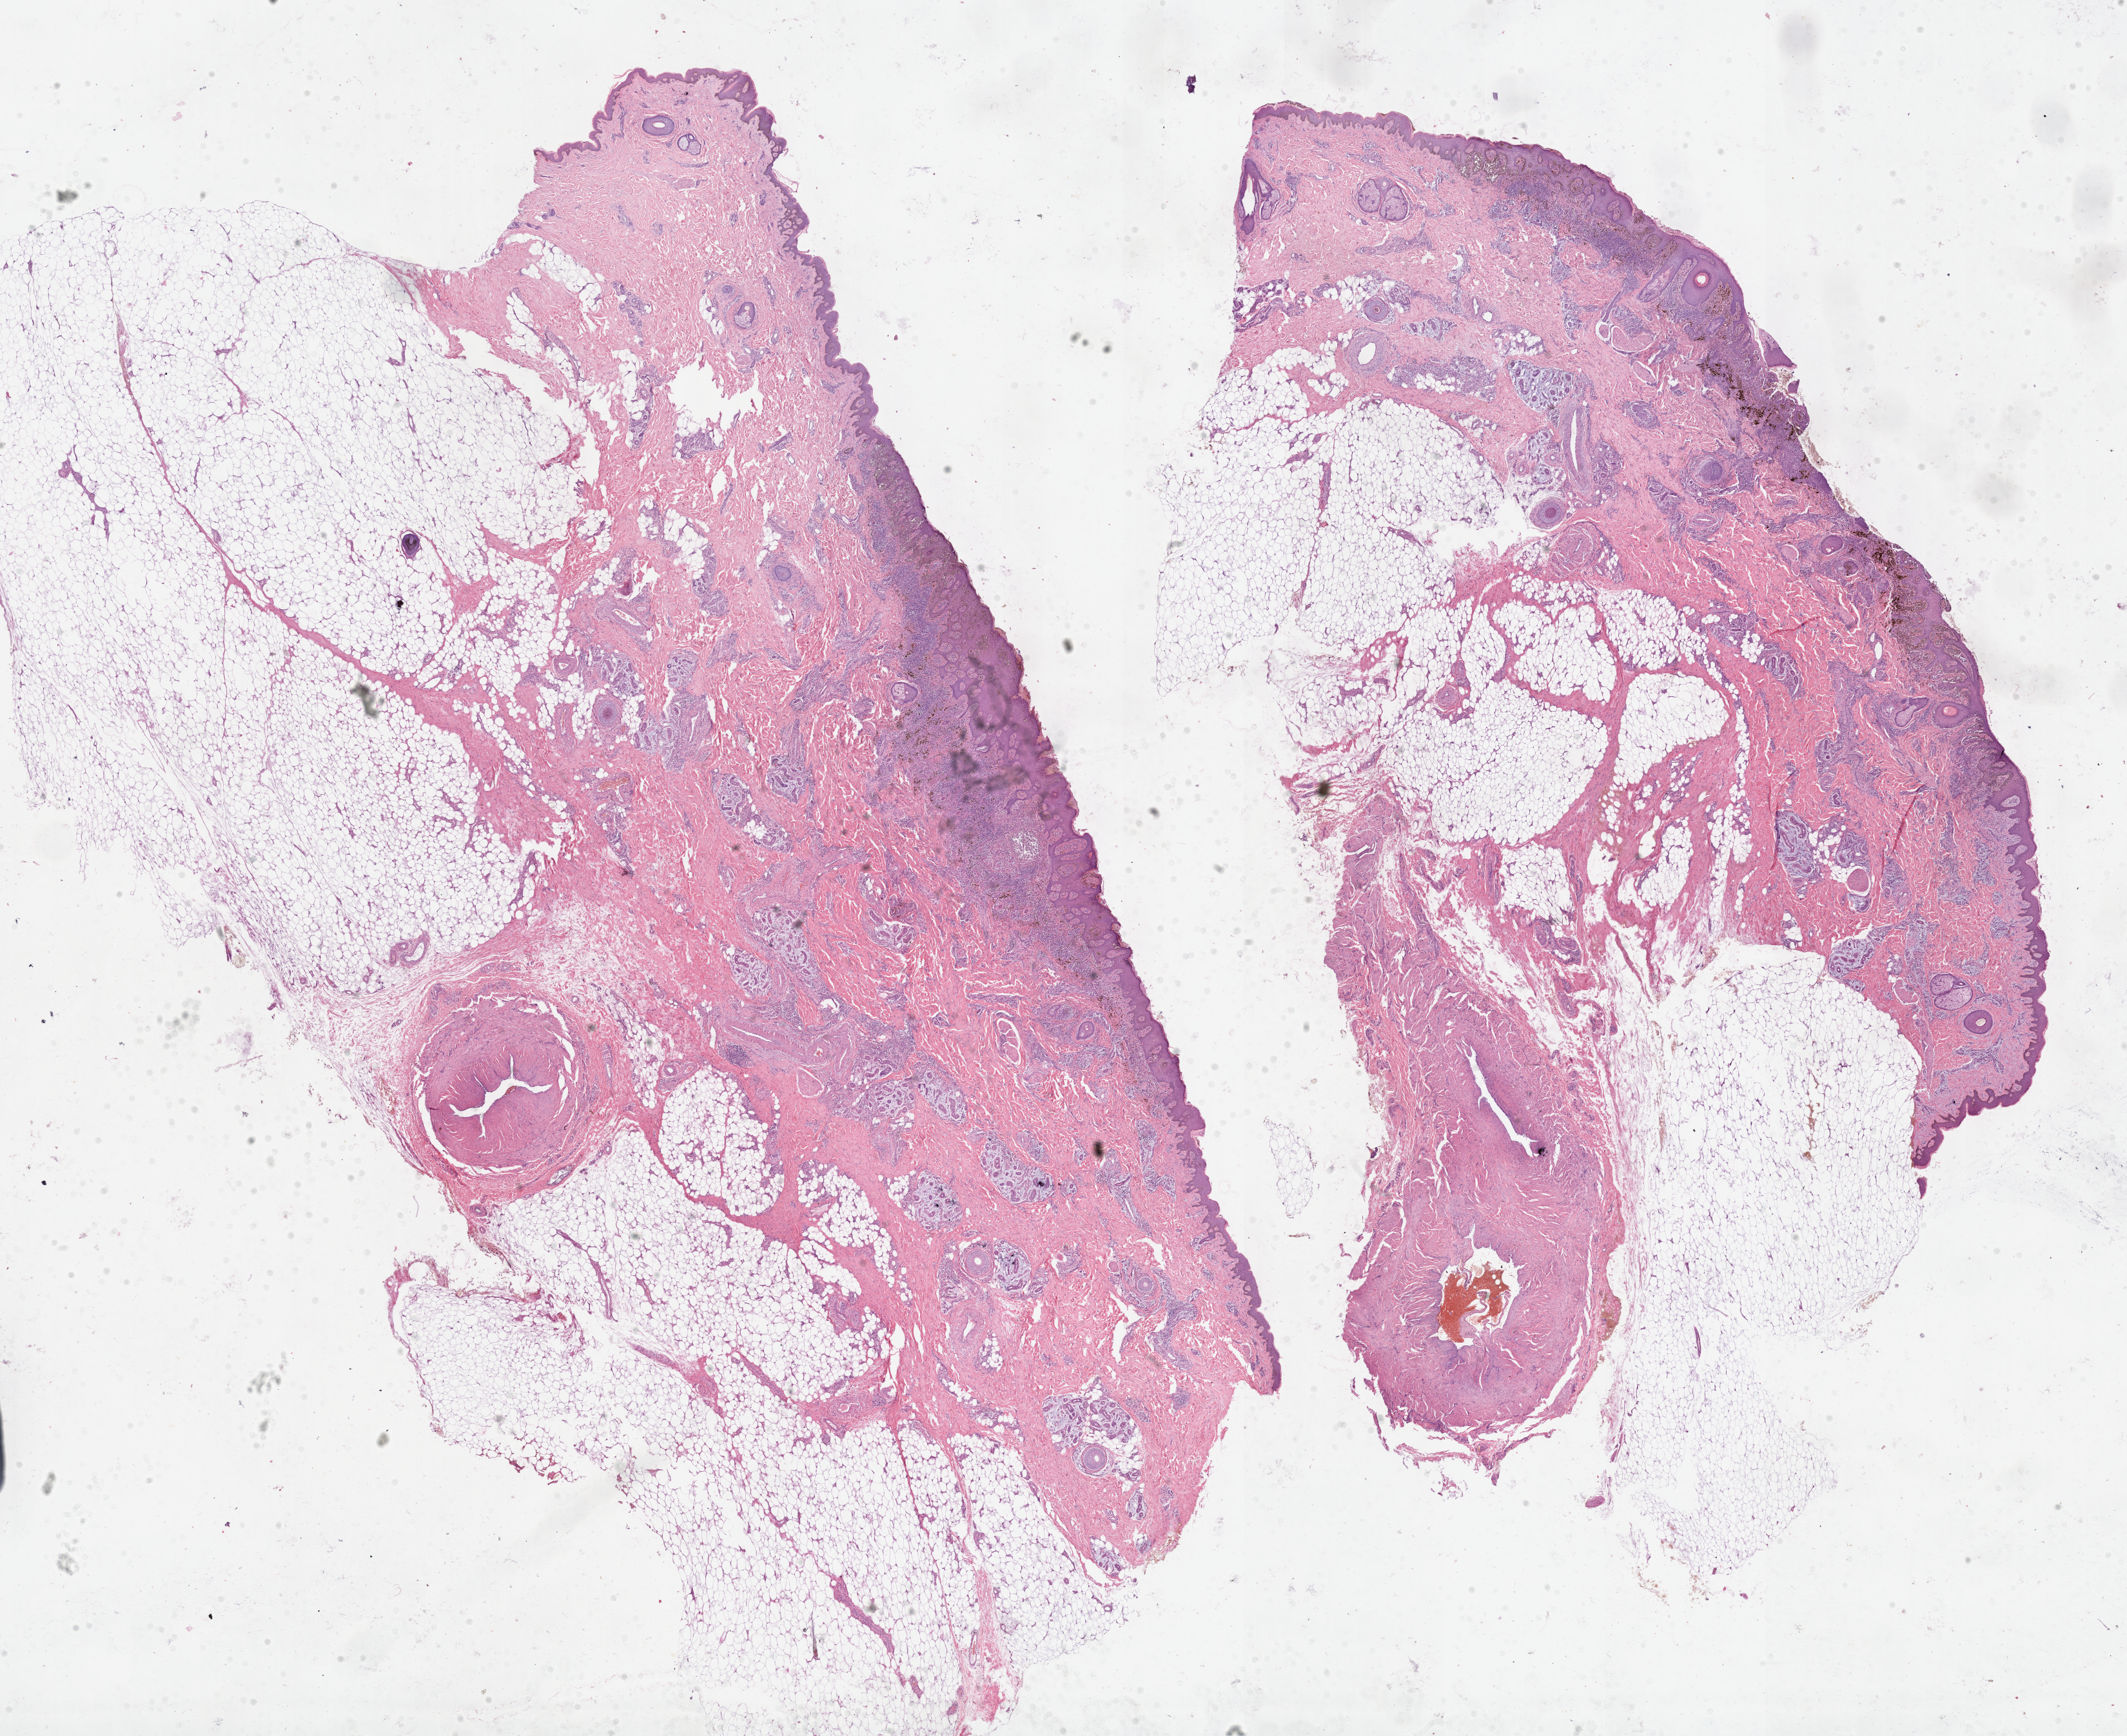
Hematoxylin and eosin (H&E) stained whole-slide image, a low-resolution overview of the entire scanned area, about 26.7 x 21.8 mm (slide scanned at 40x), FFPE section, skin, primary tumour sample. Patient: male, age at initial diagnosis 51 years.
Histologic diagnosis: Malignant melanoma, NOS.